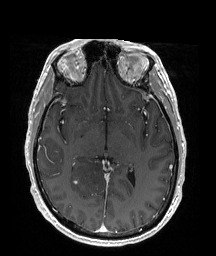
Brain MRI from a brain-tumour surgery series, one axial slice; position 102 of 176 along the scan axis; T1-weighted post-contrast; 1 mm slice thickness; 216 × 256 image matrix, field of view 211 × 250 mm. From the clinical record (not read from this slice): histopathology: Oligodendroglioma; WHO grade: 2; IDH mutation: yes; tumour location: Right Parietal.
Annotated regions visible in this slice (outlined manually by an expert reader):
- tumour: bounding box (x1, y1, x2, y2) in pixels: (70, 152, 111, 205)